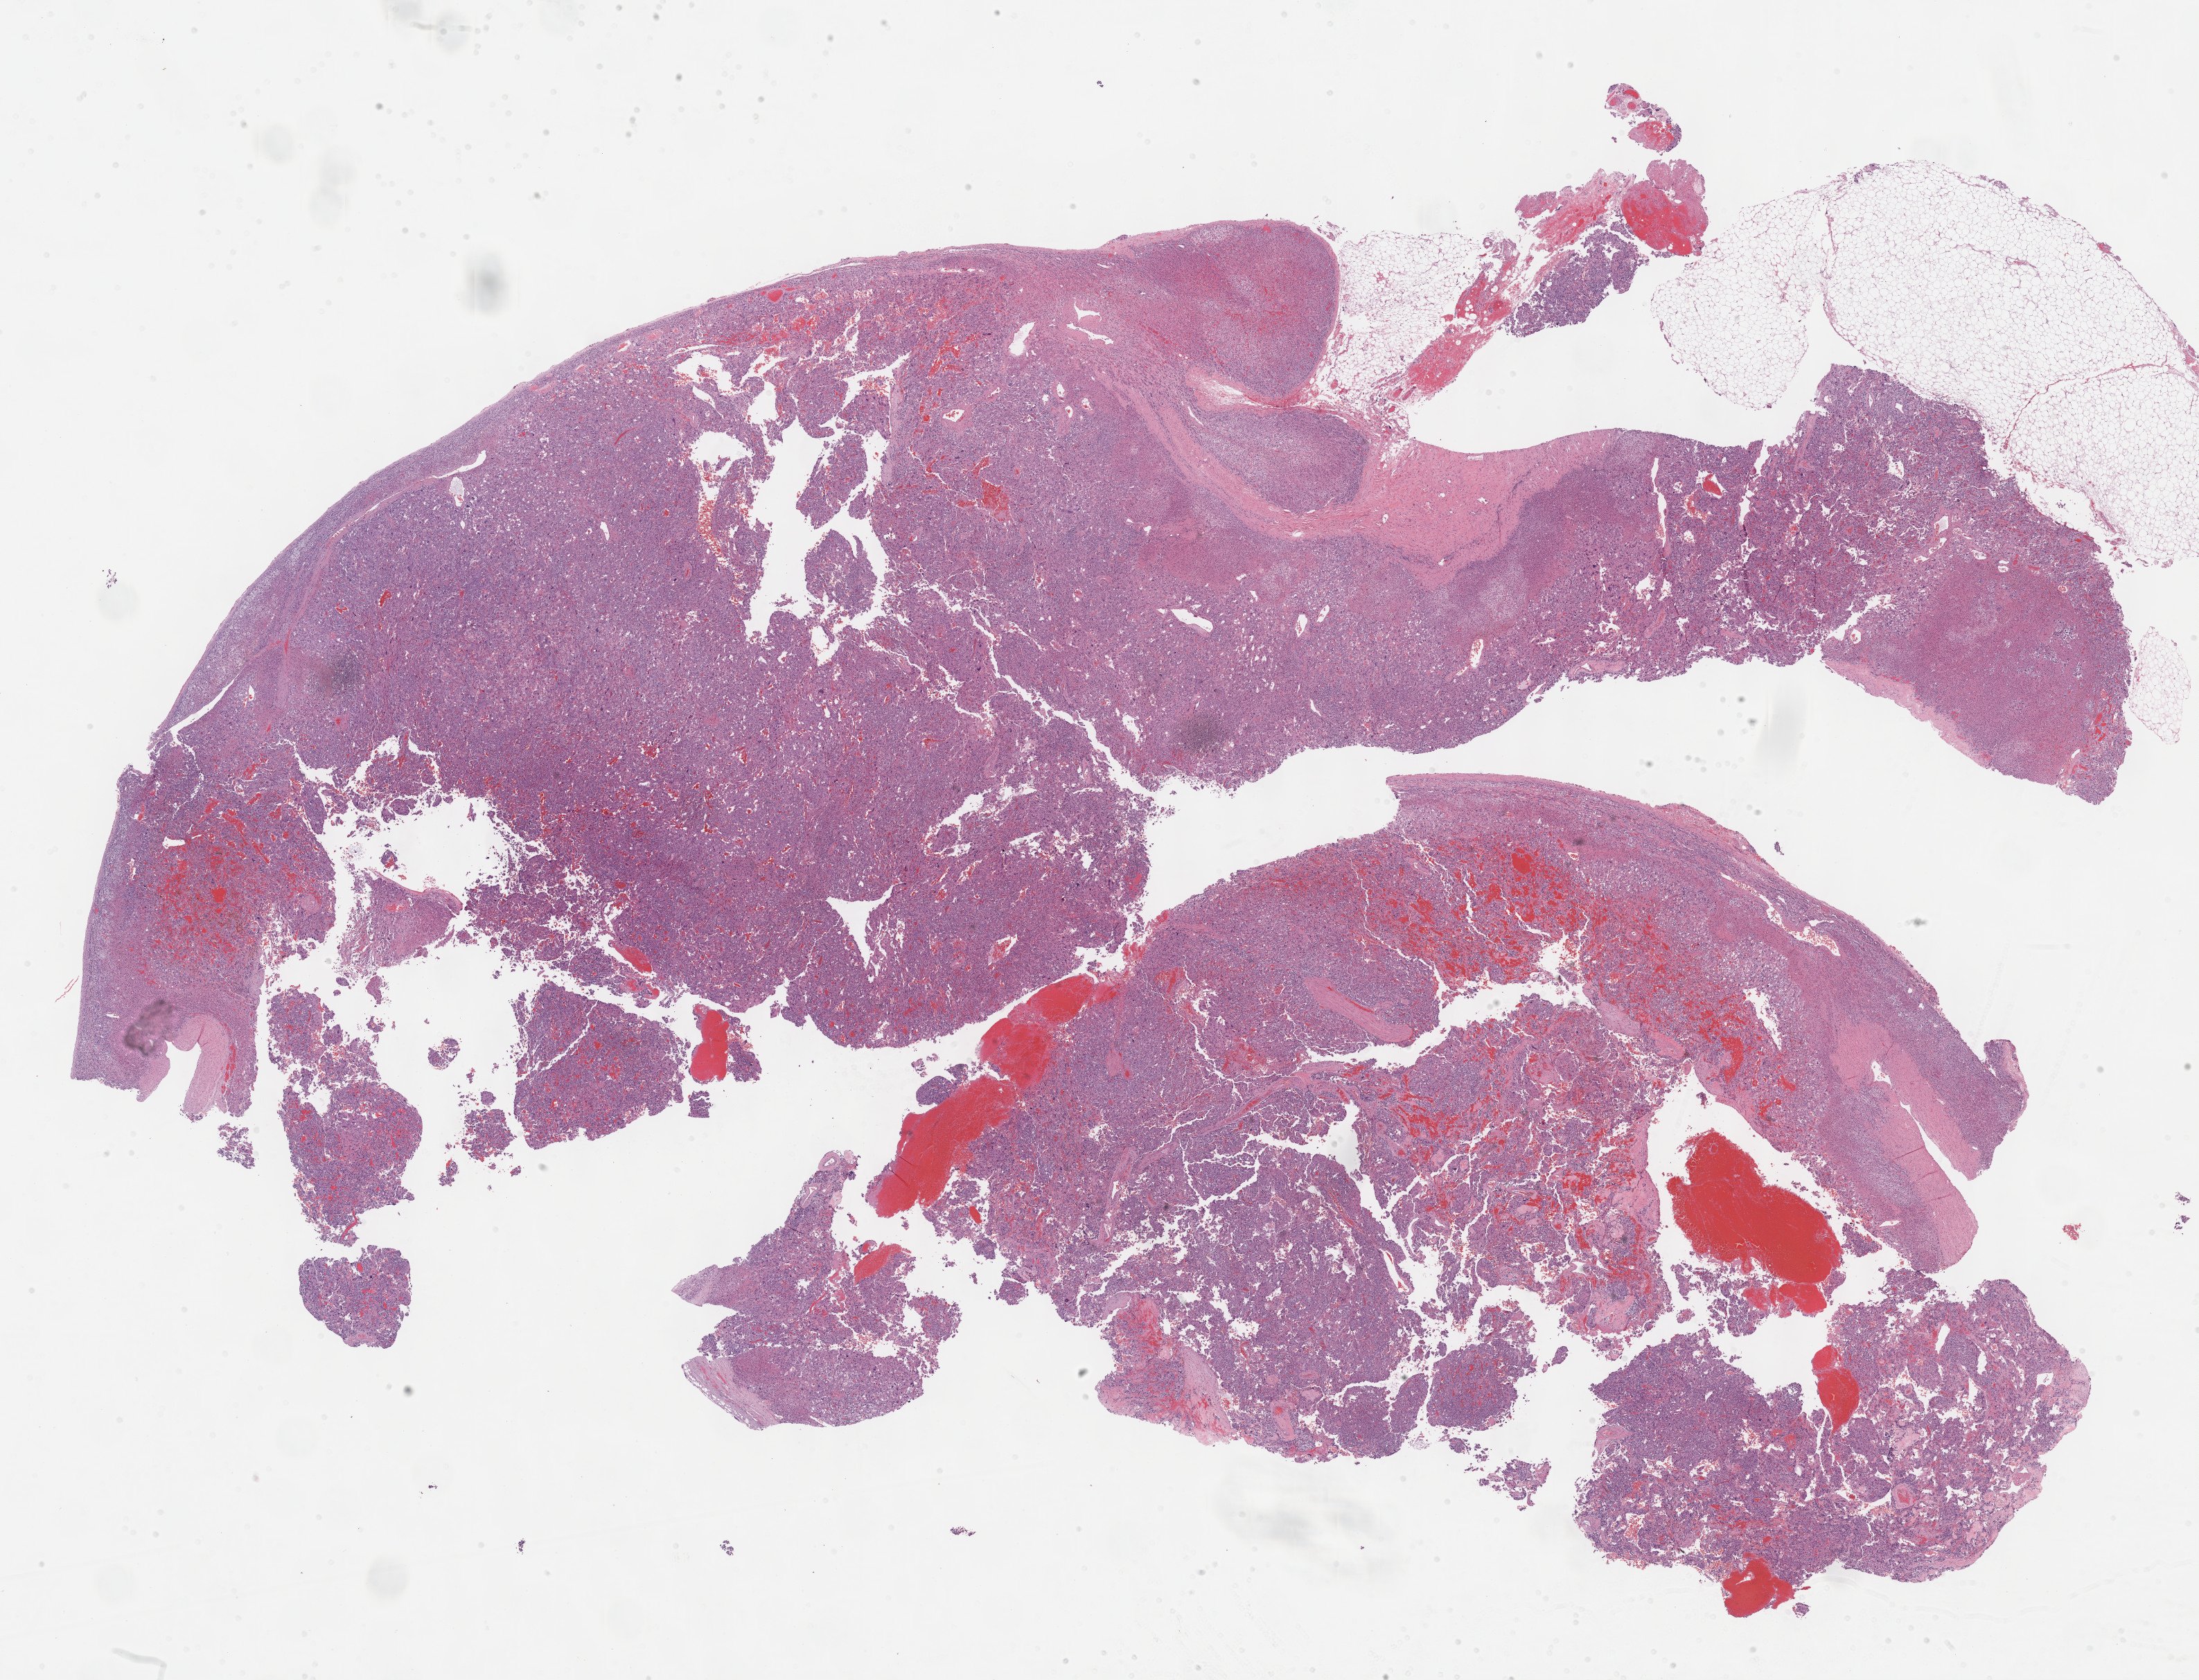
Whole-slide histology image, H&E-stained — shown as a low-resolution overview of the whole scanned area (about 25.7 x 19.6 mm, from a 40x scan). Formalin-fixed paraffin-embedded (FFPE) diagnostic section. Primary tumour sample from the adrenal gland. Female patient; age at initial diagnosis 64 years.
Histologic diagnosis: Pheochromocytoma, NOS.